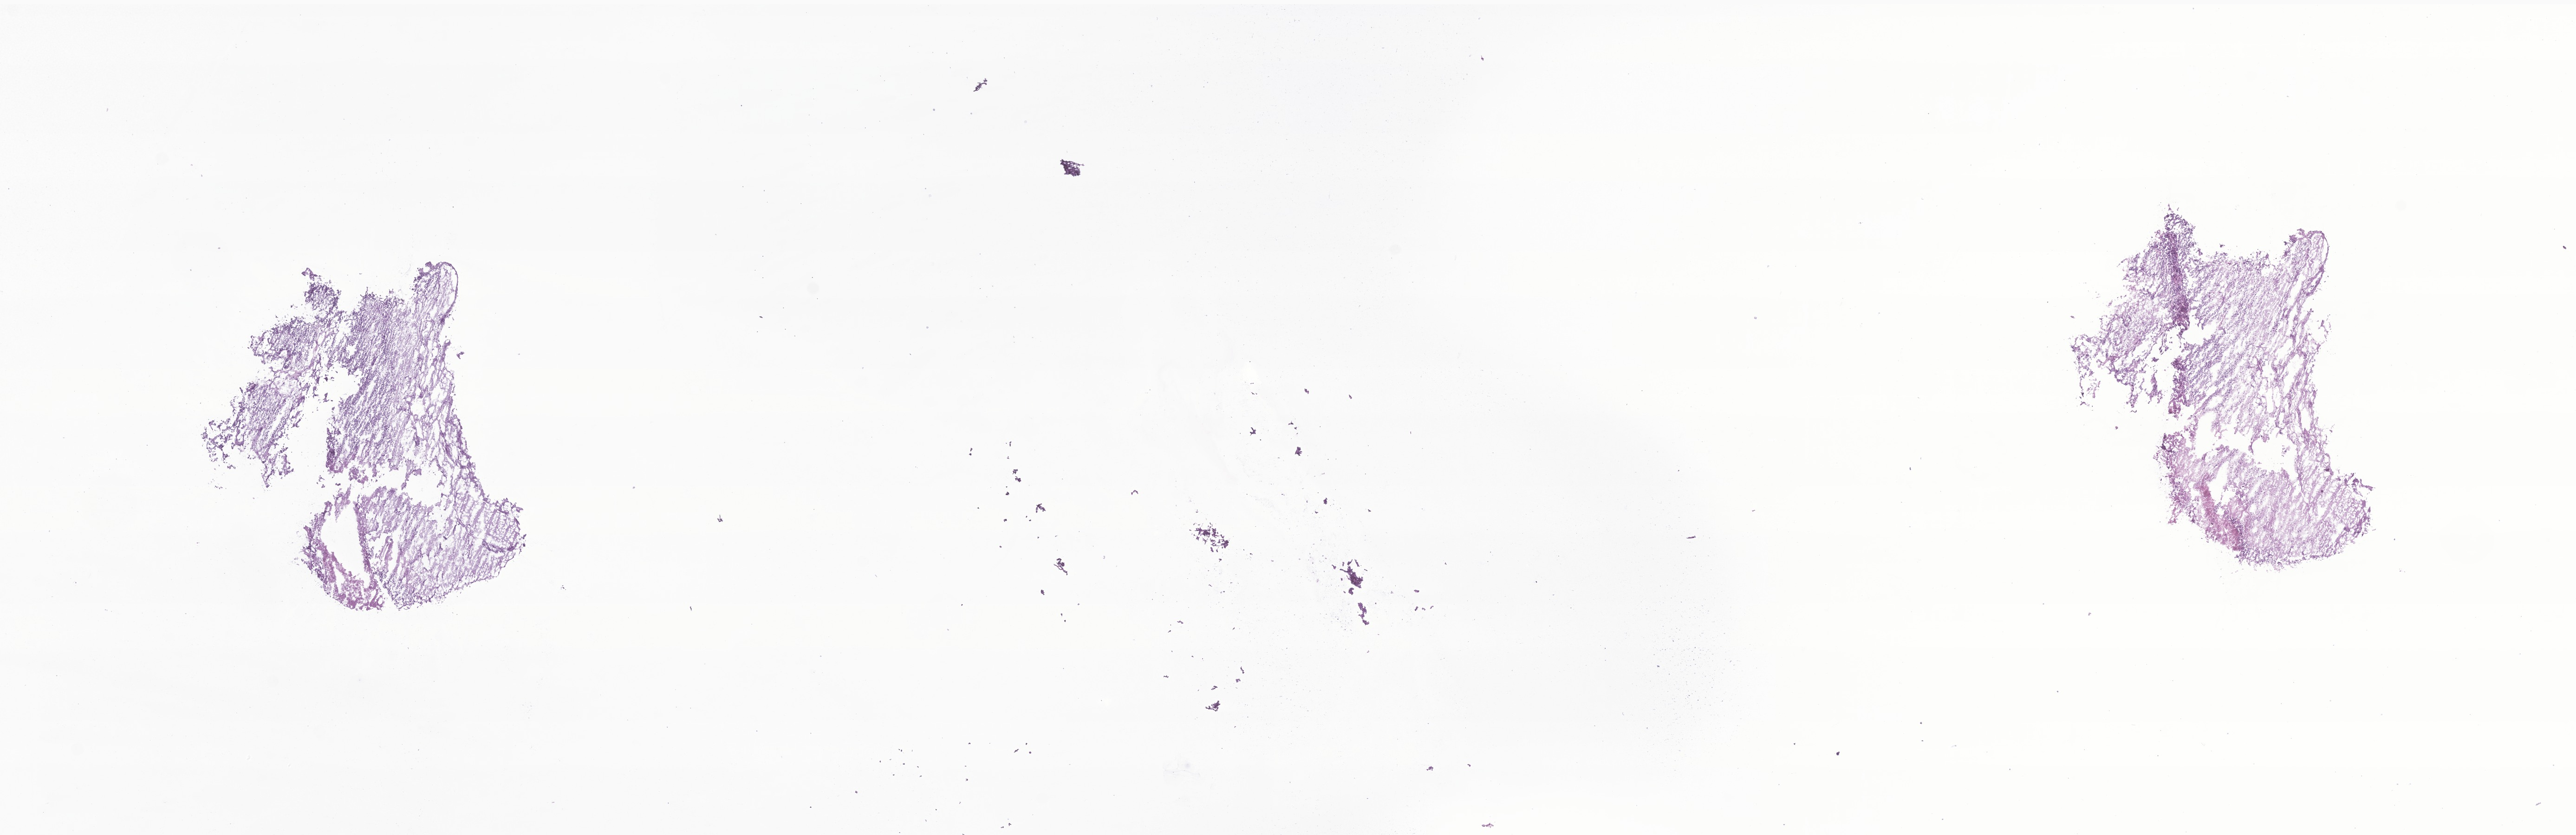
H&E whole-slide image of tumor tissue from the soft tissue of thorax, whole scanned area (about 23.4 x 7.6 mm) shown as a low-resolution overview, cryosection (OCT / tissue freezing medium). Patient: female, age 893 days (about 2.4 years).
Diagnosis (ICD-O-3 morphology term): Neuroblastoma, NOS.